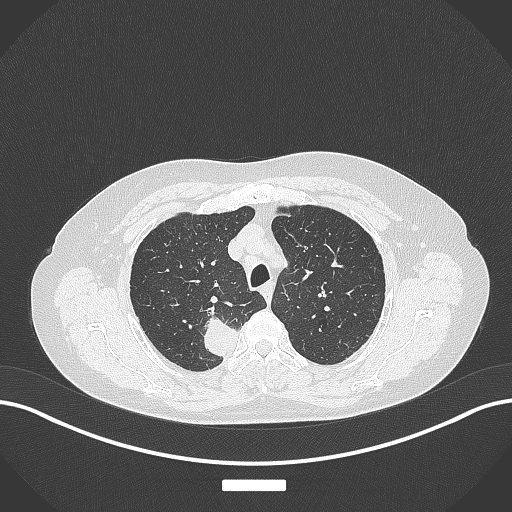
Chest CT, one axial slice. Slice 307 of 357 in the series (ordered by position). Reconstruction kernel B70f. 120 kVp. Lung window (W 1500 / L -600 HU). 1 mm slice thickness. 512 × 512 image matrix. Patient: female, 62 years. Case-level facts recorded for this patient, not image findings: clinical TNM (as recorded): T1c N1 M0.
Outlined on this slice (bounding box drawn by a radiologist):
- lung tumour (recorded histology: squamous cell carcinoma): bounding box [x1, y1, x2, y2] px = [205, 313, 242, 362]